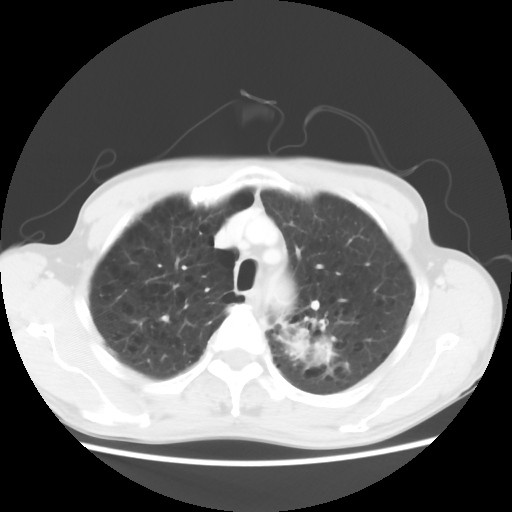
Chest CT, one axial slice. Slice 50 of 64 in the series (ordered by position). Reconstruction kernel STANDARD. Lung window (W 1500 / L -600 HU). 512 × 512 image matrix, field of view 346 × 346 mm. Male patient, age 63 years. Case-level facts recorded for this patient, not image findings: clinical TNM (as recorded): T2 N0 M0.
Outlined on this slice (bounding box drawn by a radiologist):
- lung tumour (recorded histology: adenocarcinoma): bounding box [x1, y1, x2, y2] px = [280, 325, 334, 366]